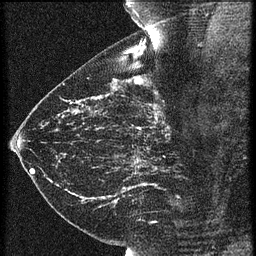
Breast MRI (dynamic contrast-enhanced), one sagittal slice; slice 35 of 60 in the series (ordered by position); 3 images stored at this slice position (order not interpretable as contrast timing); 1.5 T; TE 4.2 ms, TR 21.3 ms; 256 × 256 image matrix, field of view 180 × 180 mm. Patient: female, 43 years. Case-level facts recorded for this patient, not image findings: setting: breast cancer imaged before/during neoadjuvant chemotherapy; receptor status: HER2-positive.
Structures marked on this image (semi-automatic segmentation, software-assisted and operator-edited):
- analysis volume of interest (the breast-tissue region the enhancement analysis was run in; not a lesion): bounding box (x1, y1, x2, y2) in pixels: (119, 114, 189, 173)
- tumour enhancement mask (voxels above the 90 % enhancement threshold inside the analysis volume of interest): (138, 114, 161, 129)